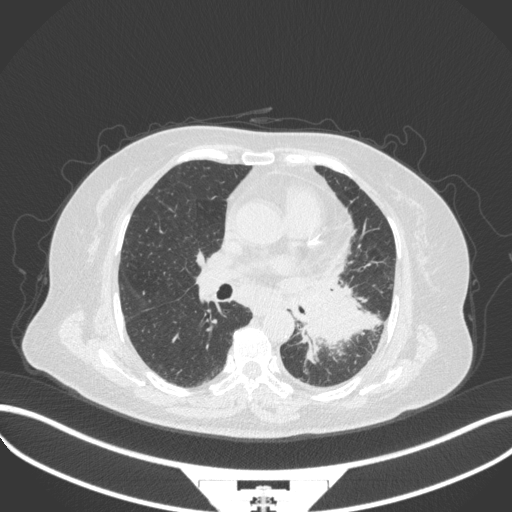
Chest CT, one axial slice; slice 183 of 328 in the series (ordered by position); reconstruction kernel B31f; 120 kVp; lung window (W 1500 / L -600 HU); 1 mm slice thickness; 512 × 512 image matrix, field of view 400 × 400 mm. Patient: female, 69 years. From the clinical record (not read from this slice): clinical TNM (as recorded): T2b N3 M1.
Structures marked on this image (bounding box drawn by a radiologist):
- lung tumour (recorded histology: adenocarcinoma): bounding box (x1, y1, x2, y2) in pixels: (298, 280, 379, 353)